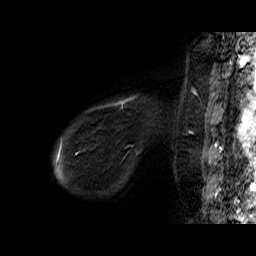
Breast MRI (dynamic contrast-enhanced), one sagittal slice; position 5 of 60 along the scan axis; dynamic contrast-enhanced series, time point 2 of 6 at this slice position (early post-contrast); 1.5 T; TE 6.4 ms, TR 32.9 ms; 4 mm slice thickness; 256 × 256 image matrix, field of view 200 × 200 mm. Female patient. Case-level facts recorded for this patient, not image findings: setting: breast cancer imaged before/during neoadjuvant chemotherapy; receptor status: HER2-positive.
Annotated regions visible in this slice (semi-automatic segmentation, software-assisted and operator-edited):
- analysis volume of interest (the breast-tissue region the enhancement analysis was run in; not a lesion): box from (x=71, y=95) to (x=155, y=146) px
- tumour enhancement mask (voxels above the 100 % enhancement threshold inside the analysis volume of interest): (x=86, y=96)–(x=136, y=113)